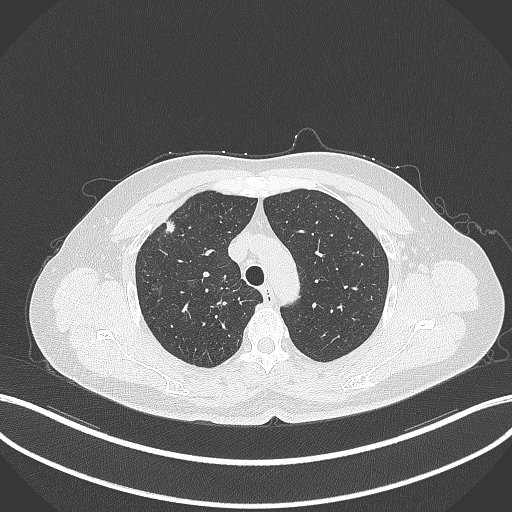
Chest CT, one axial slice; position 281 of 353 along the scan axis; reconstruction kernel B70f; lung window (W 1500 / L -600 HU); 512 × 512 image matrix, field of view 400 × 400 mm. Female patient, age 56 years. From the clinical record (not read from this slice): clinical TNM (as recorded): T1c N0 M0.
Structures marked on this image (rectangle marked by the reading radiologist):
- lung tumour (recorded histology: adenocarcinoma): bounding box (x1, y1, x2, y2) in pixels: (162, 218, 179, 238)